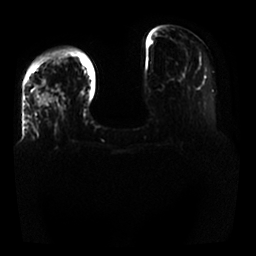
Breast MRI, one axial slice; slice 6 of 25 in the series (ordered by position); diffusion-weighted series; image 2 of 4 stored at this slice position (different b-values; order by instance number); 1.5 T; 4 mm slice thickness; 256 × 256 image matrix. Female patient.
Annotated regions visible in this slice (expert manual segmentation):
- tumour on diffusion-weighted imaging: bounding box <37,52,66,107> (left, top, right, bottom; pixels)